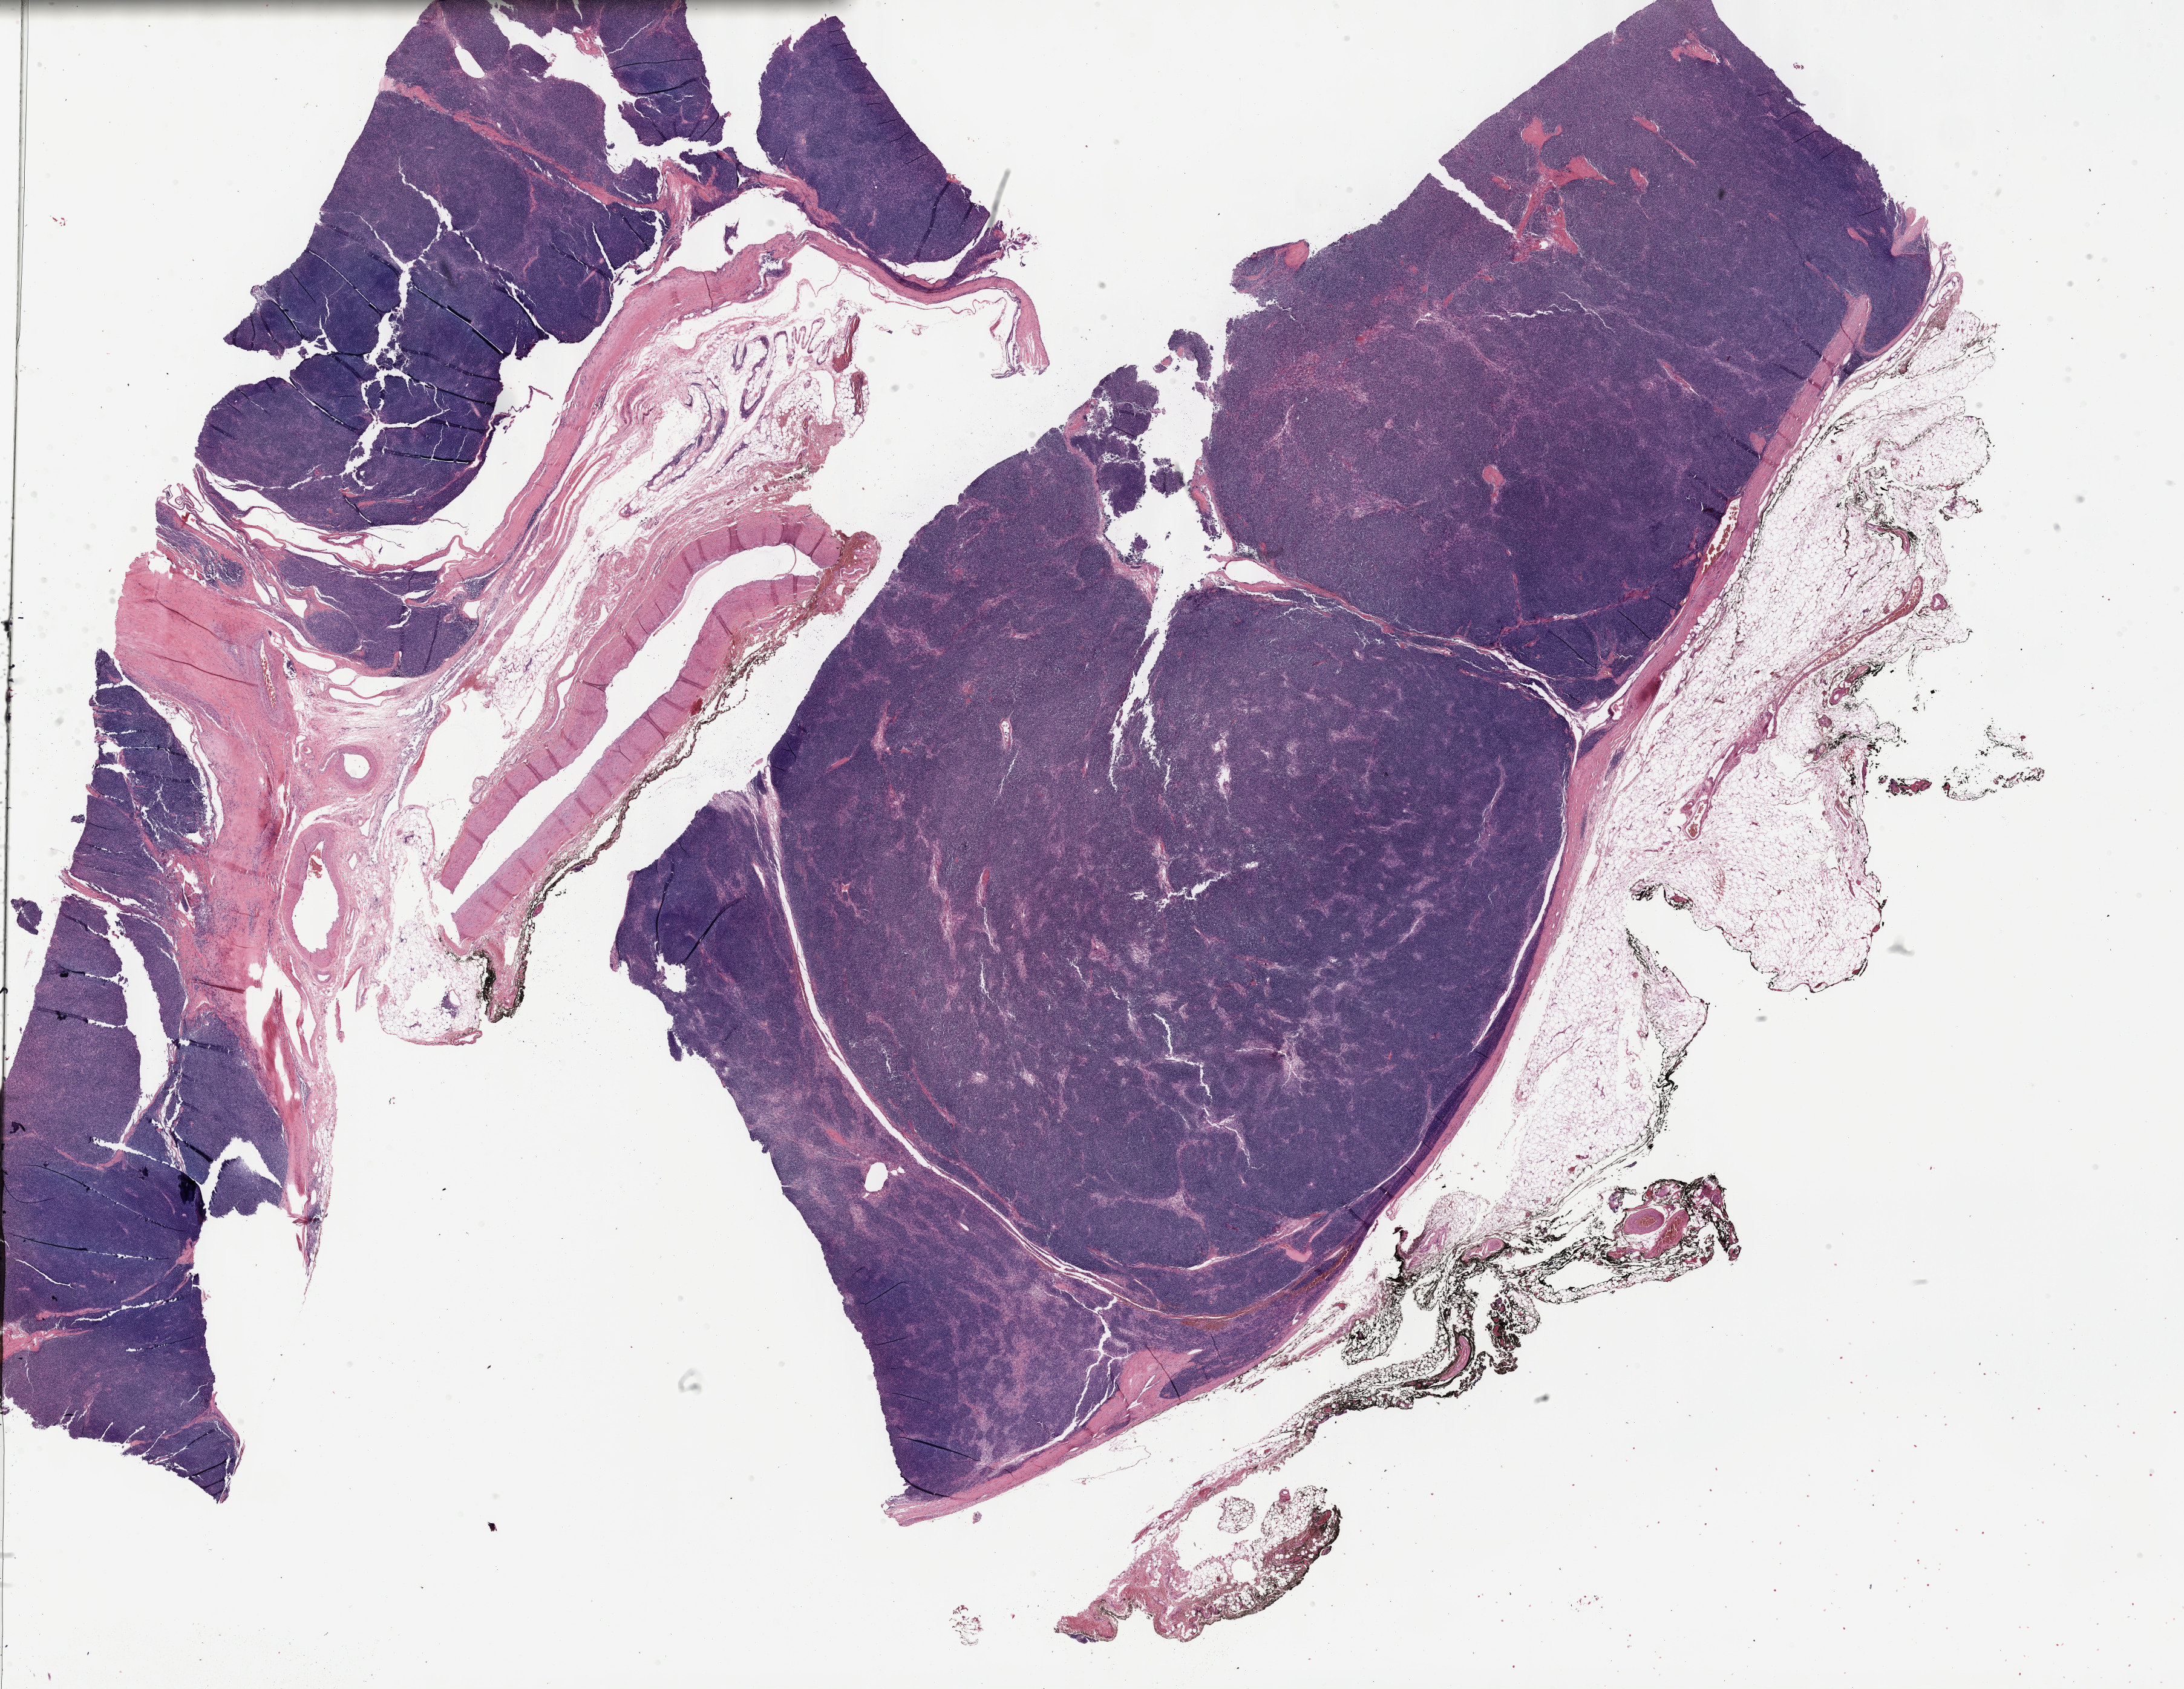
Digitized H&E tissue section (whole slide), low-resolution overview of the scanned area, about 29.2 x 22.6 mm. FFPE section. Thymus, primary tumour sample. Patient: female, age at initial diagnosis 50 years.
• histologic diagnosis: Thymoma, type AB, NOS (anterior mediastinum)